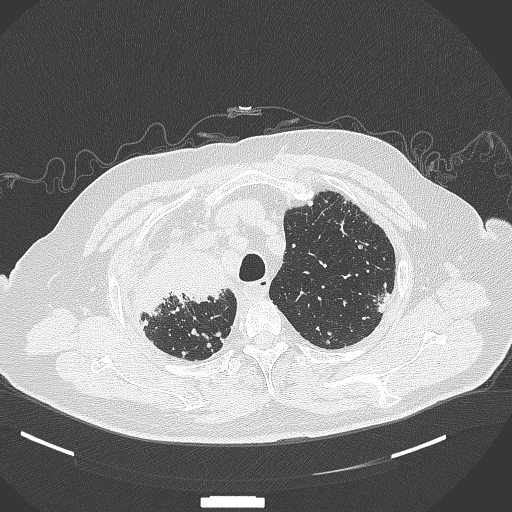
Chest CT, one axial slice. 120 kVp. Lung window (W 1500 / L -600 HU). 1 mm slice thickness. 512 × 512 image matrix. Patient: male, 69 years. From the clinical record (not read from this slice): clinical TNM (as recorded): T4 N3 M1.
Outlined on this slice (rectangle marked by the reading radiologist):
- lung tumour (recorded histology: adenocarcinoma): box from (x=140, y=248) to (x=230, y=317) px